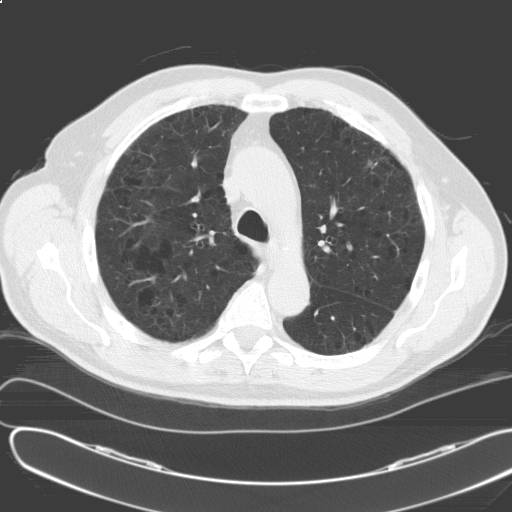
Low-dose screening chest CT, axial slice. Baseline annual screen. Lung window (W 1500 / L -600 HU). Standard (soft-tissue) reconstruction kernel (C). Slice 115 of 164 in the series. 512 × 512 image matrix. Male participant, aged 69 years at enrolment. Former smoker at enrolment.
- Expert reader's lesion annotation, bounding box (x1, y1, x2, y2) in pixels: (121, 149, 158, 181).
- The screening reader recorded 2 non-calcified nodules or masses ≥4 mm on this exam (left upper lobe, right lower lobe); which of them this box marks is not recorded.
- Later outcome: lung cancer diagnosed 450 days after this screen (after the second annual screen) — adenosquamous carcinoma, right upper lobe, poorly differentiated (G3), stage IV (AJCC 6th edition), 30 mm at pathology.